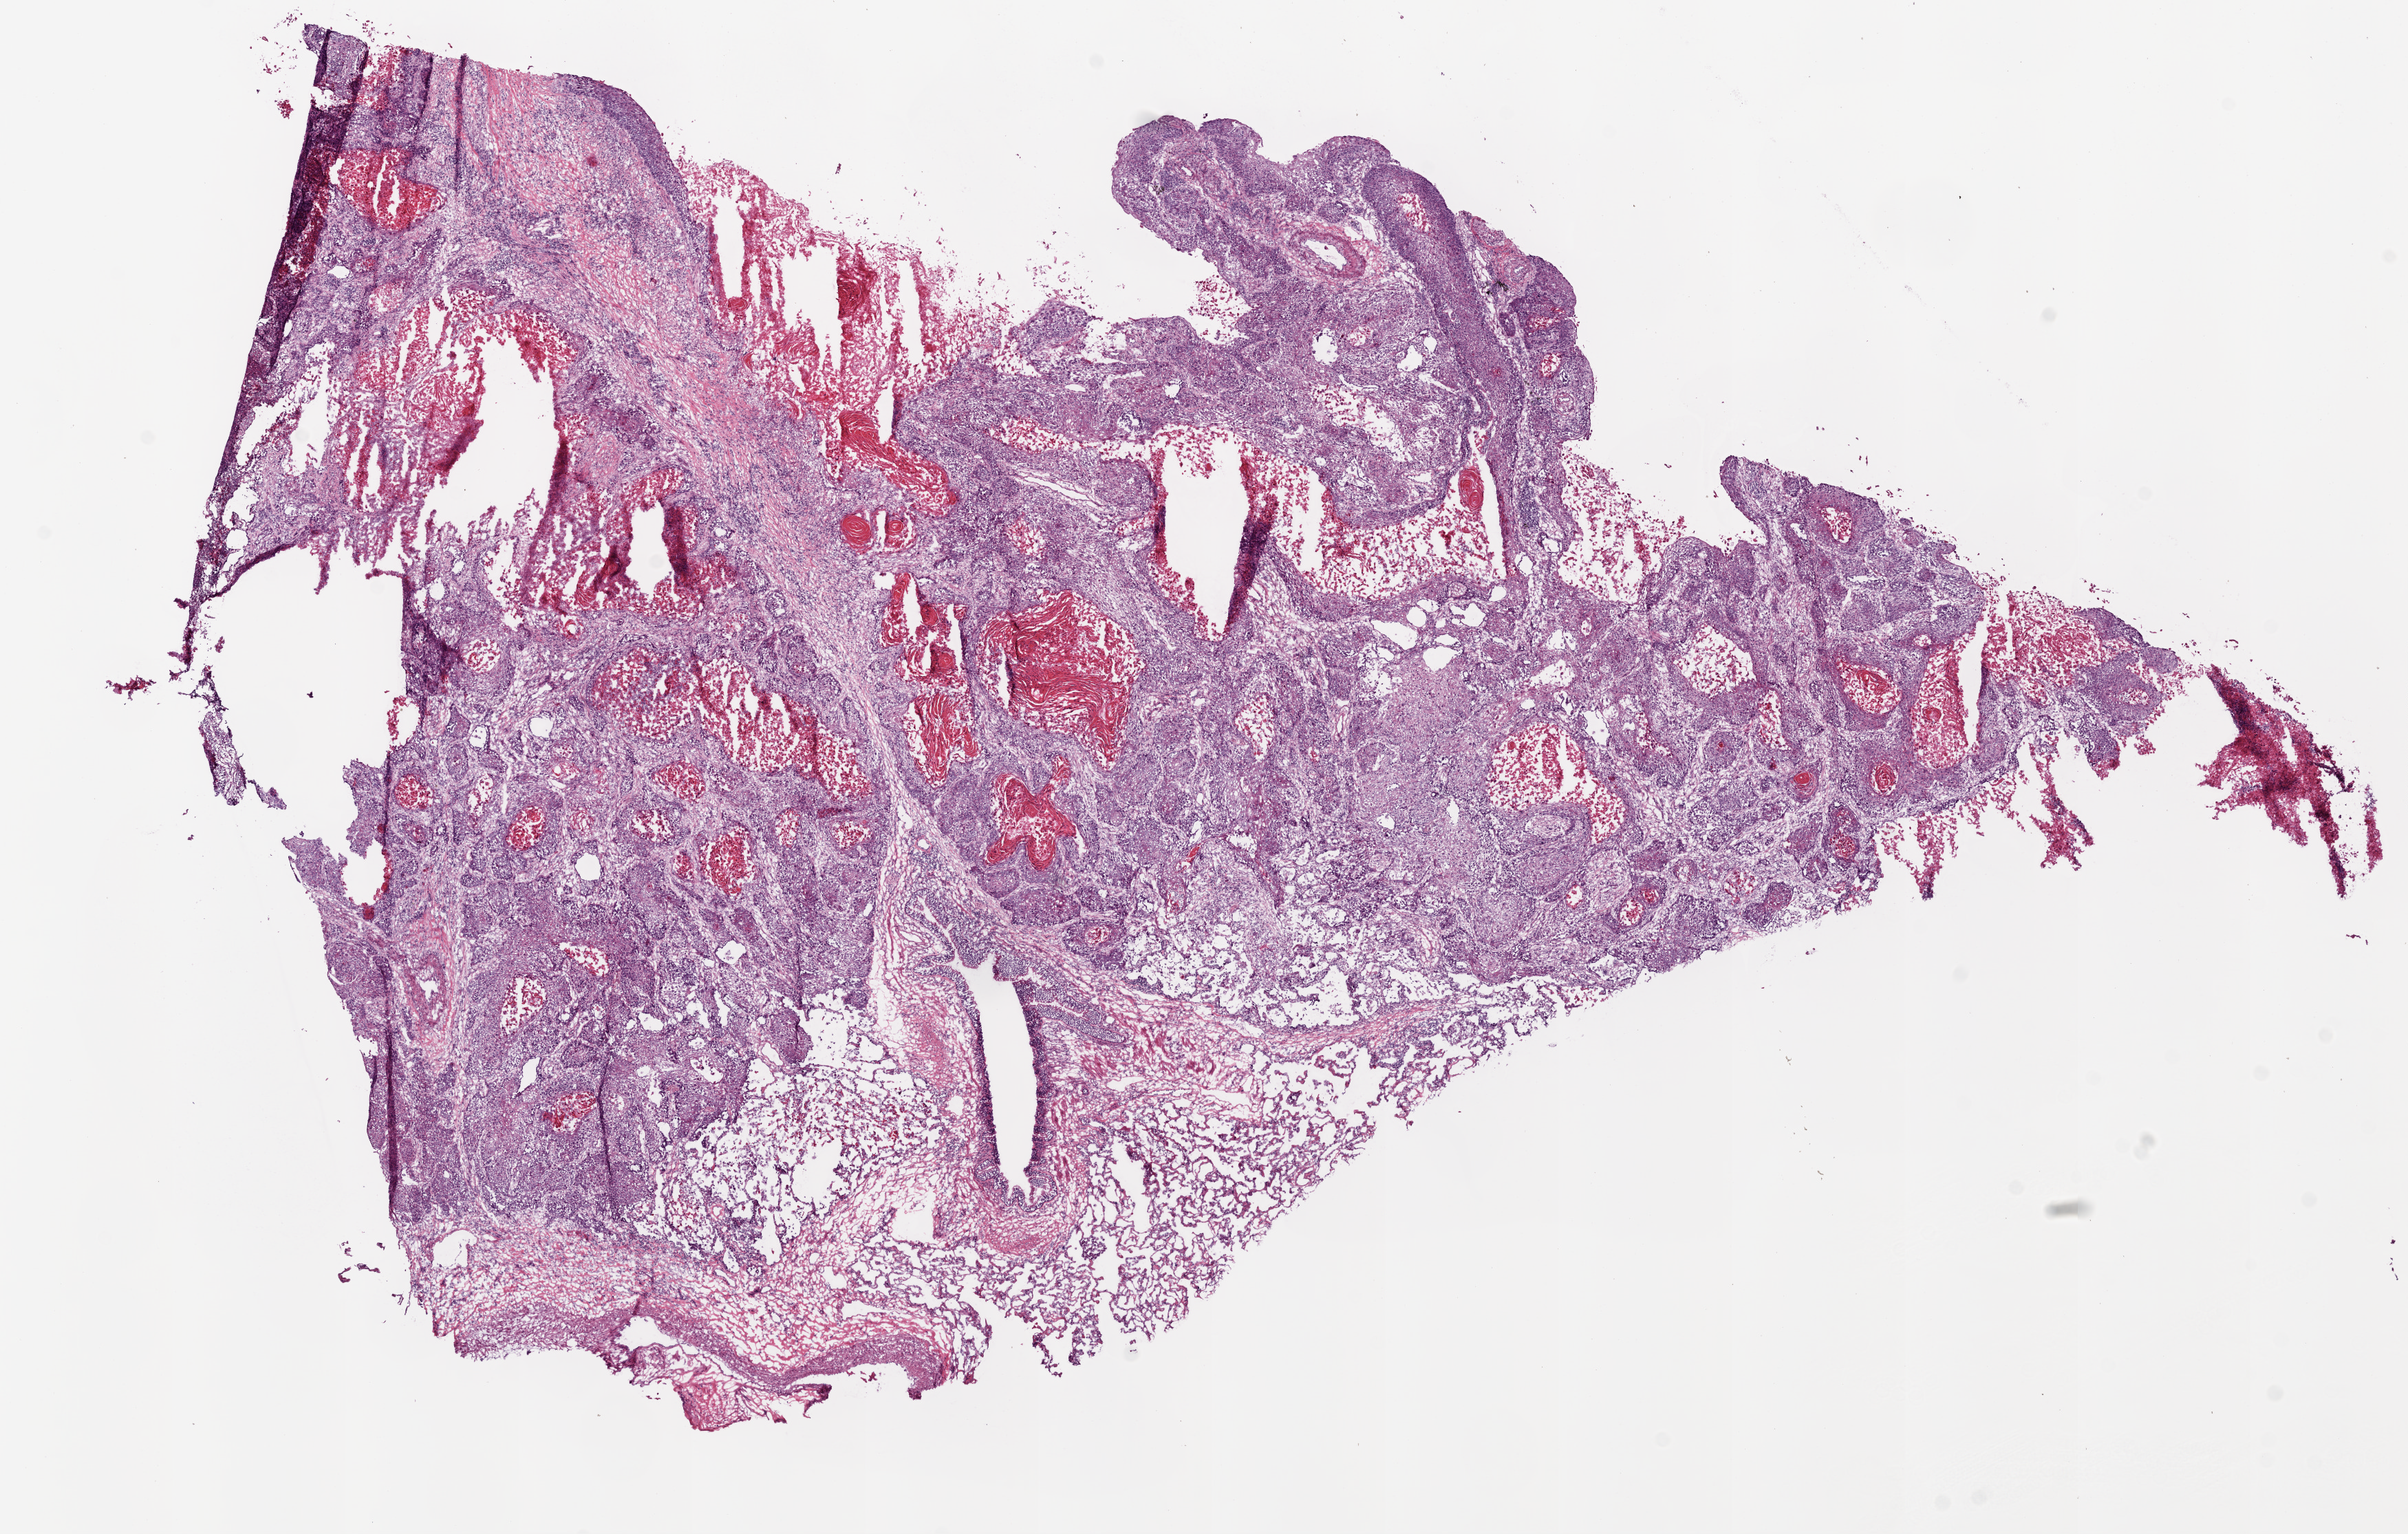
Hematoxylin and eosin (H&E) stained whole-slide image, a low-resolution overview of the entire scanned area, about 14.0 x 8.9 mm. Frozen section. Lung, primary tumour sample. Female, age 78 years at initial diagnosis. Composition of this section per pathologist review: tumour cells 30%, tumour nuclei 75%, normal cells 10%, stromal cells 20%, necrosis 40%.
Pathologic diagnosis: Squamous cell carcinoma, large cell, nonkeratinizing, NOS (upper lobe, lung). AJCC pathologic stage: IB (6th edition). Laterality: right.